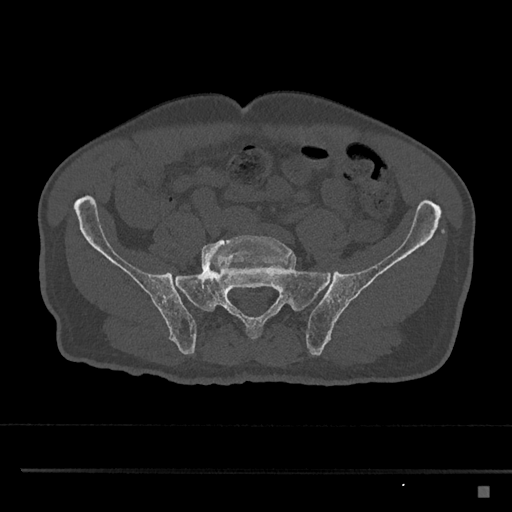
CT including the spine, one axial slice; bone window (W 1800 / L 400 HU); 0.5 mm slice thickness; 512 × 512 image matrix, field of view 391 × 391 mm. Male patient, age 59 years. From the clinical record (not read from this slice): primary cancer: prostate.
Structures marked on this image (semi-automatic segmentation, software-assisted and operator-edited):
- L5 vertebra: bounding box <201,235,292,273> (left, top, right, bottom; pixels)